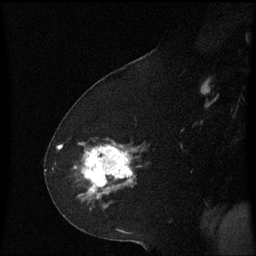
Breast MRI (dynamic contrast-enhanced), one sagittal slice; position 33 of 60 along the scan axis; dynamic contrast-enhanced series, image 2 of 3 at this slice position (ordered by acquisition); 1.5 T; TE 4.2 ms, TR 8.4 ms; 256 × 256 image matrix, field of view 200 × 200 mm. Female patient, age 60 years. Case-level facts recorded for this patient, not image findings: setting: breast cancer imaged before/during neoadjuvant chemotherapy; receptor status: triple-negative.
Annotated regions visible in this slice (semi-automatic segmentation, software-assisted and operator-edited):
- analysis volume of interest (the breast-tissue region the enhancement analysis was run in; not a lesion): bounding box (x1, y1, x2, y2) in pixels: (74, 142, 140, 211)
- tumour enhancement mask (voxels above the 70 % enhancement threshold inside the analysis volume of interest): (82, 146, 136, 195)